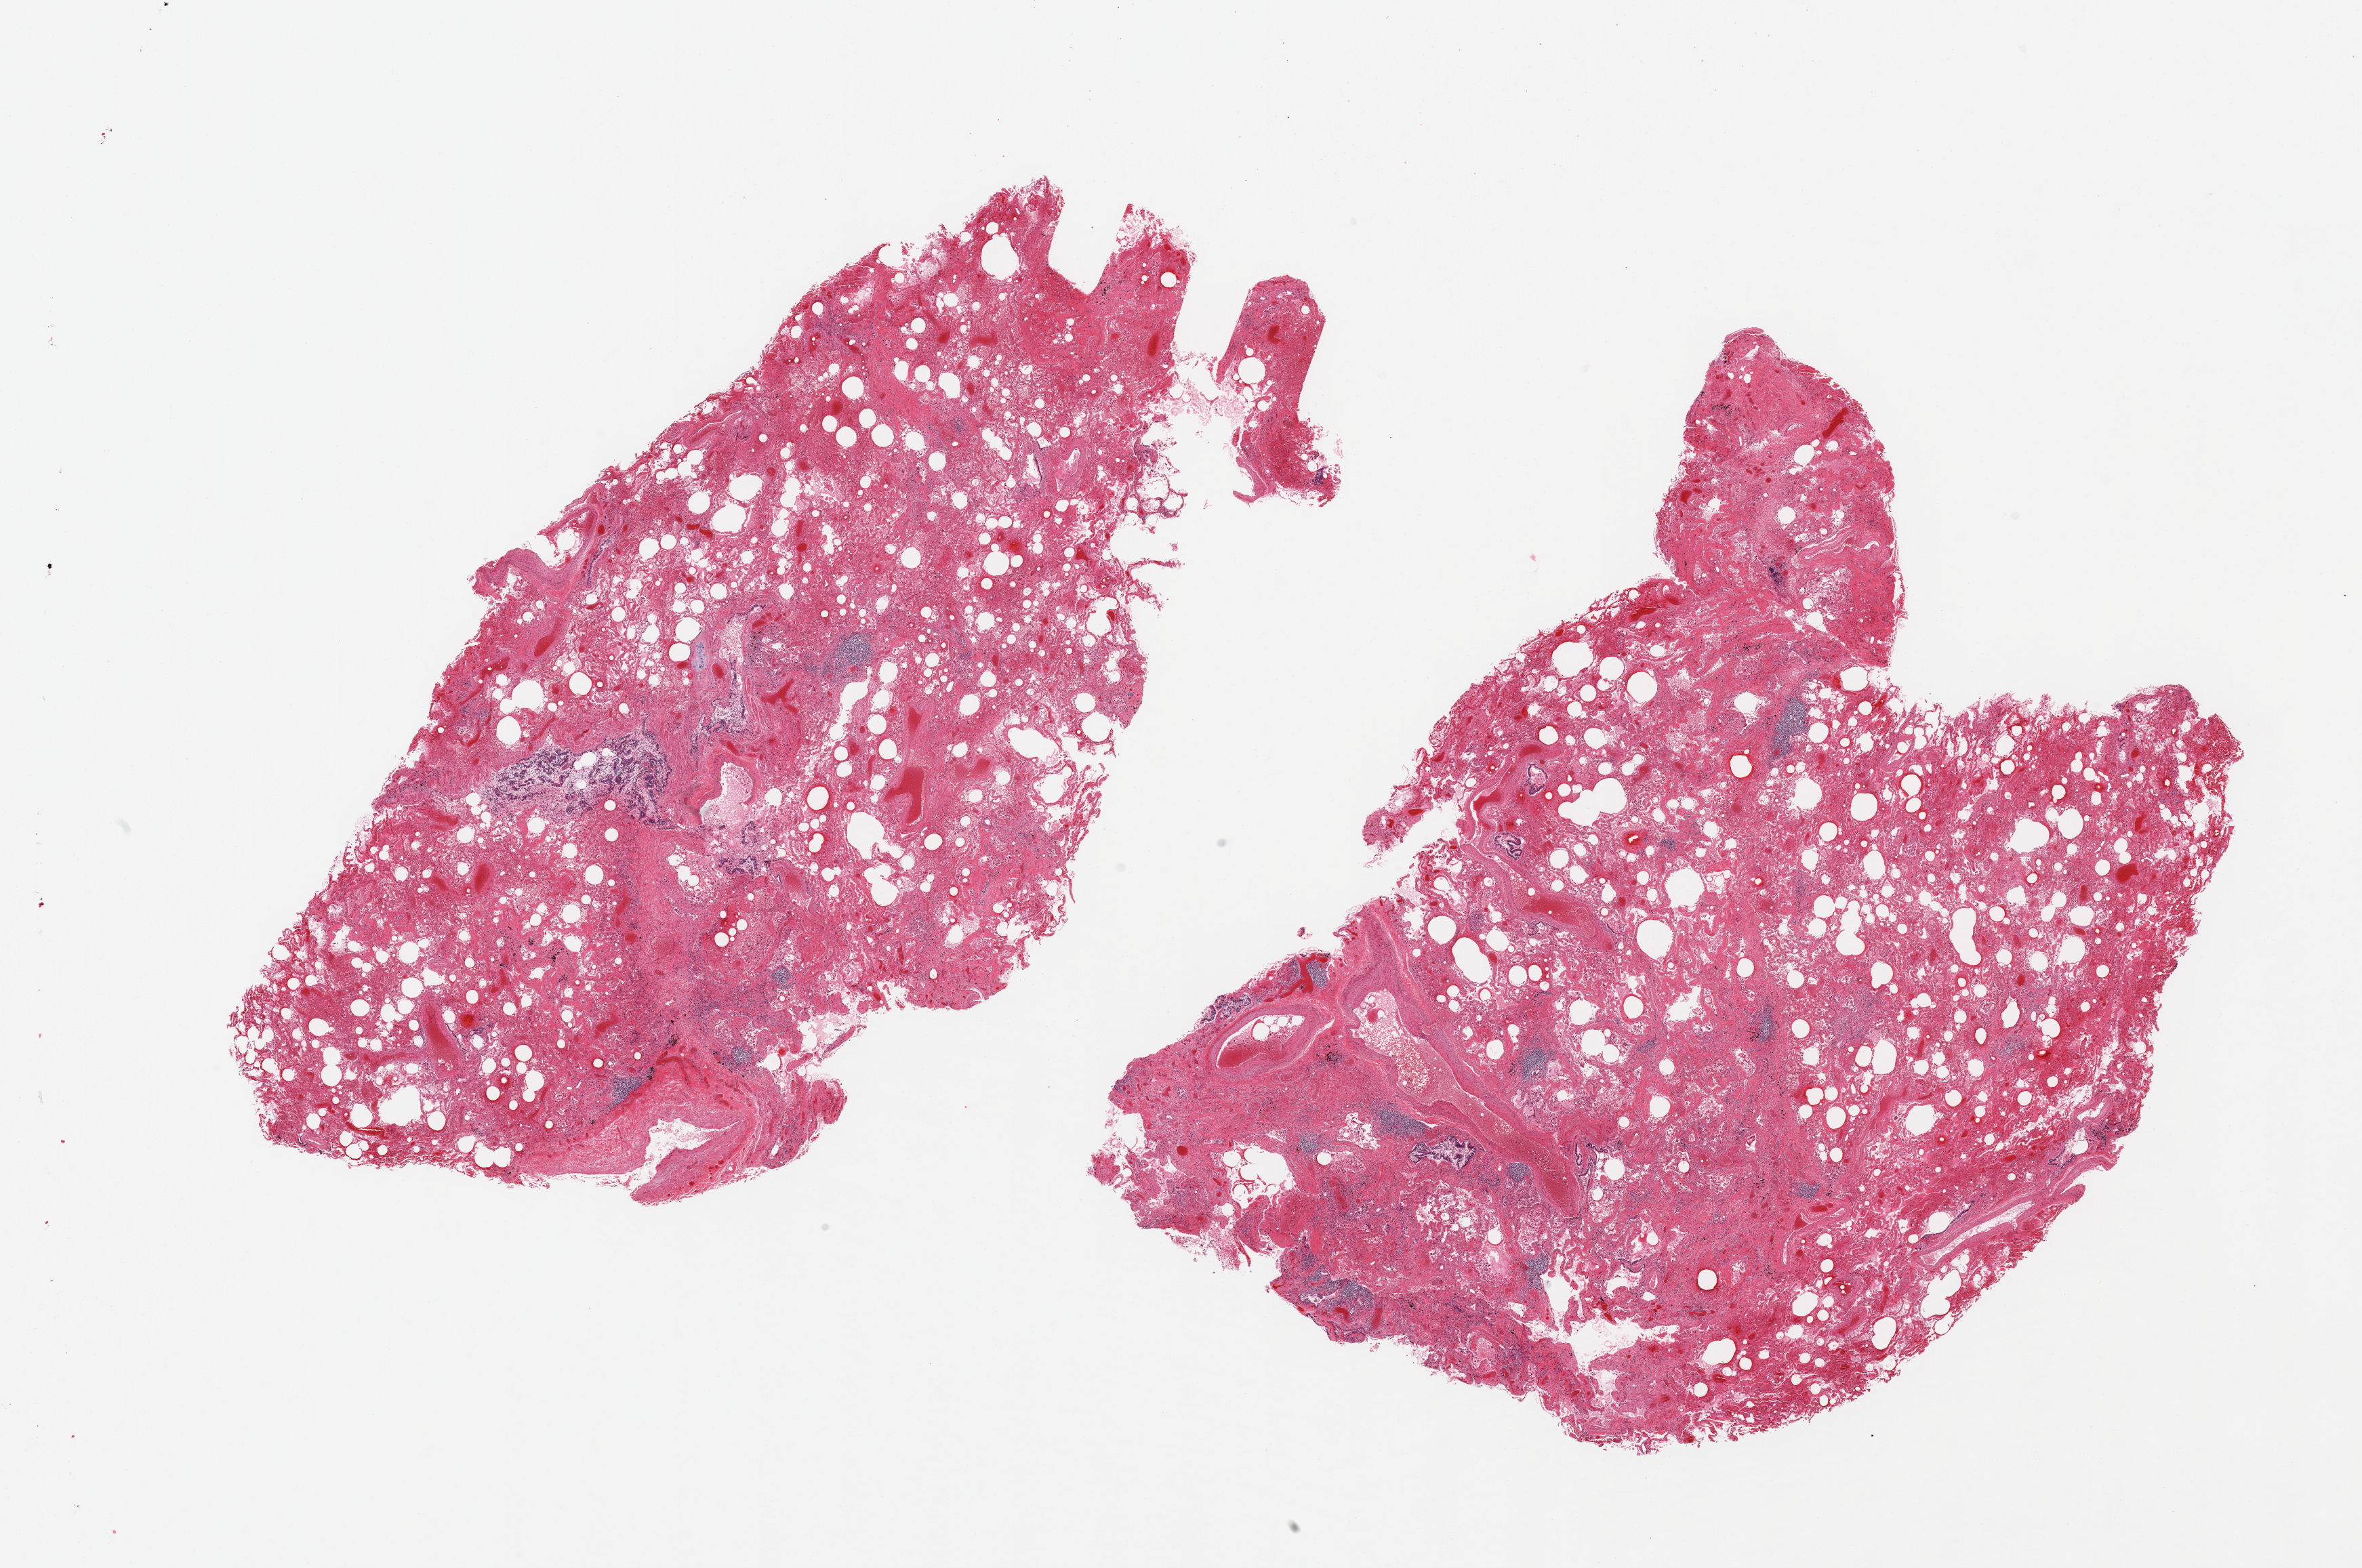
H&E whole-slide image — shown as a low-resolution overview of the whole scanned area (about 27.6 x 18.3 mm), PAXgene-fixed, paraffin-embedded tissue, target tissue: lung, donor tissue sample. Male donor.
* review note (as recorded): 2 pieces, moderate- marked congestion, focal chronic pneumonitis